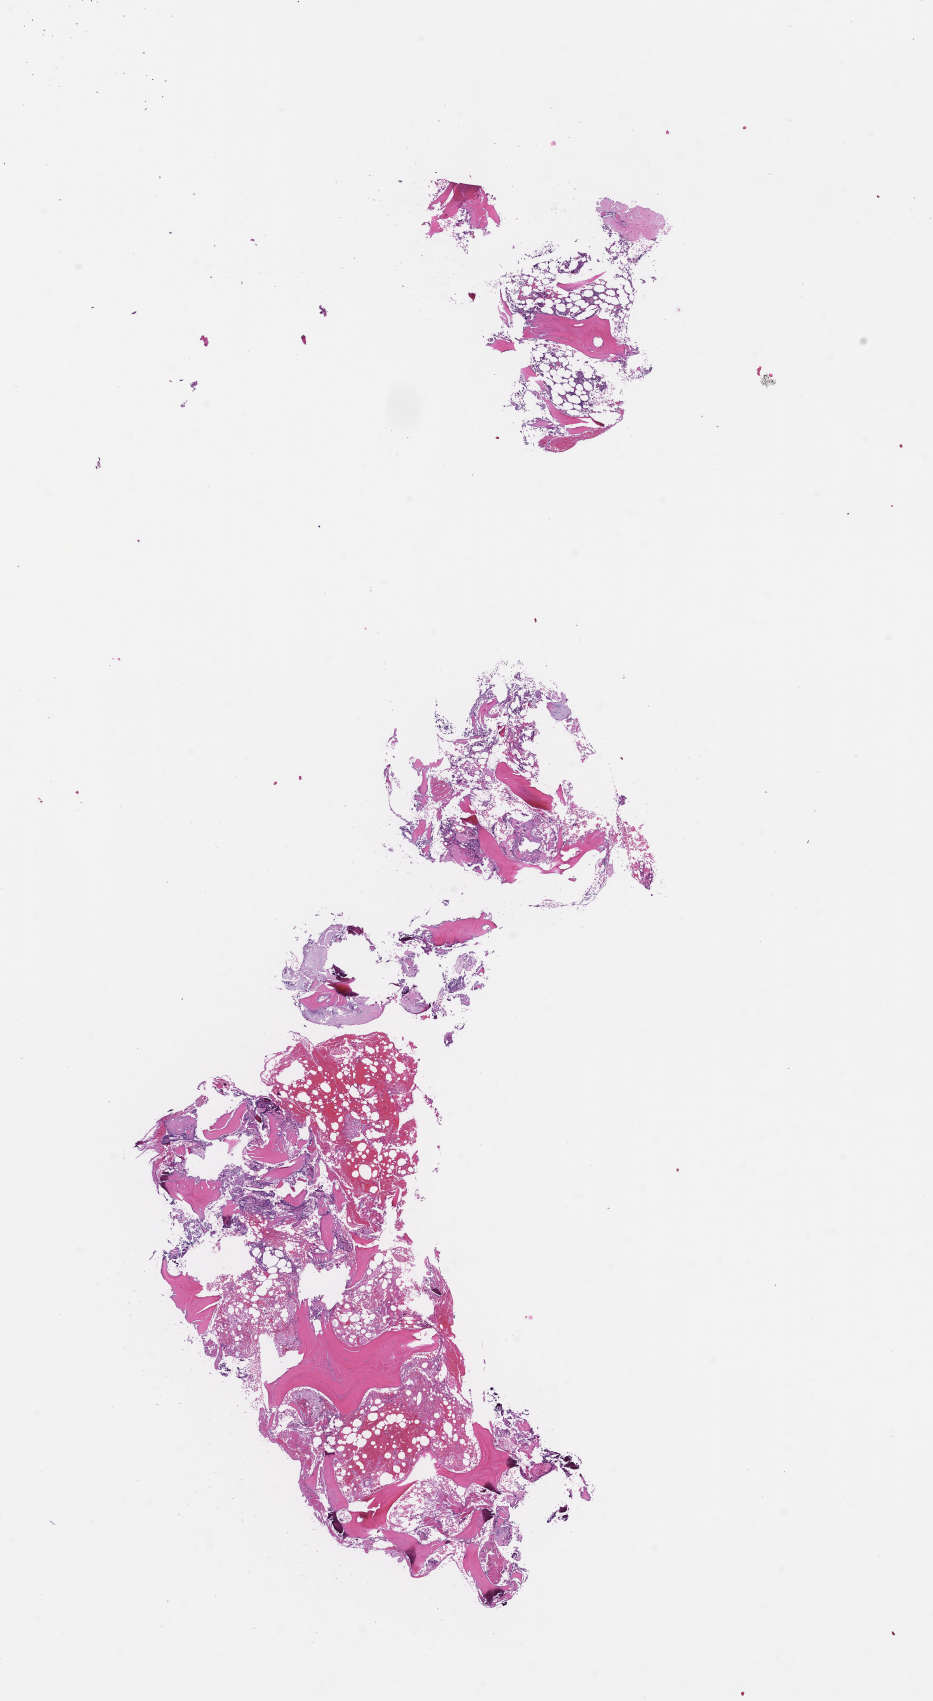
Hematoxylin and eosin (H&E) whole-slide image — low-resolution overview of the scanned area, about 7.5 x 13.7 mm, formalin-fixed, paraffin-embedded (FFPE) tissue, site: bone marrow. Patient: female.
This section: primary tumor. Diagnosis: Plasma Cell Myeloma.